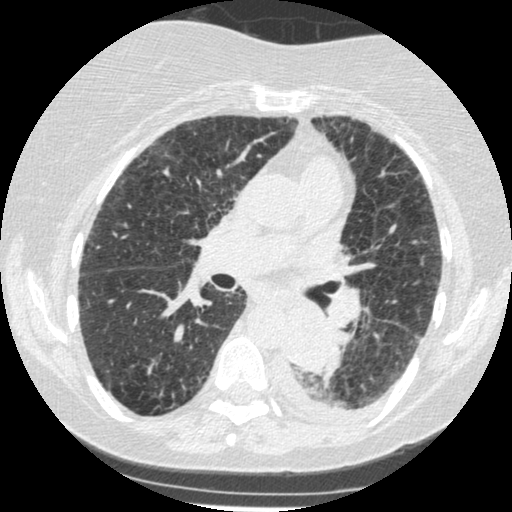
Low-dose screening chest CT, one axial slice. Slice 141 of 341 in the series (ordered by position). Reconstruction kernel STANDARD. 120 kVp. Lung window (W 1500 / L -600 HU). 512 × 512 image matrix, field of view 310 × 310 mm.
Structures marked on this image (manually delineated by an expert):
- lesion 1 (tumor, lower lobe of left lung): box from (x=285, y=307) to (x=338, y=373) px